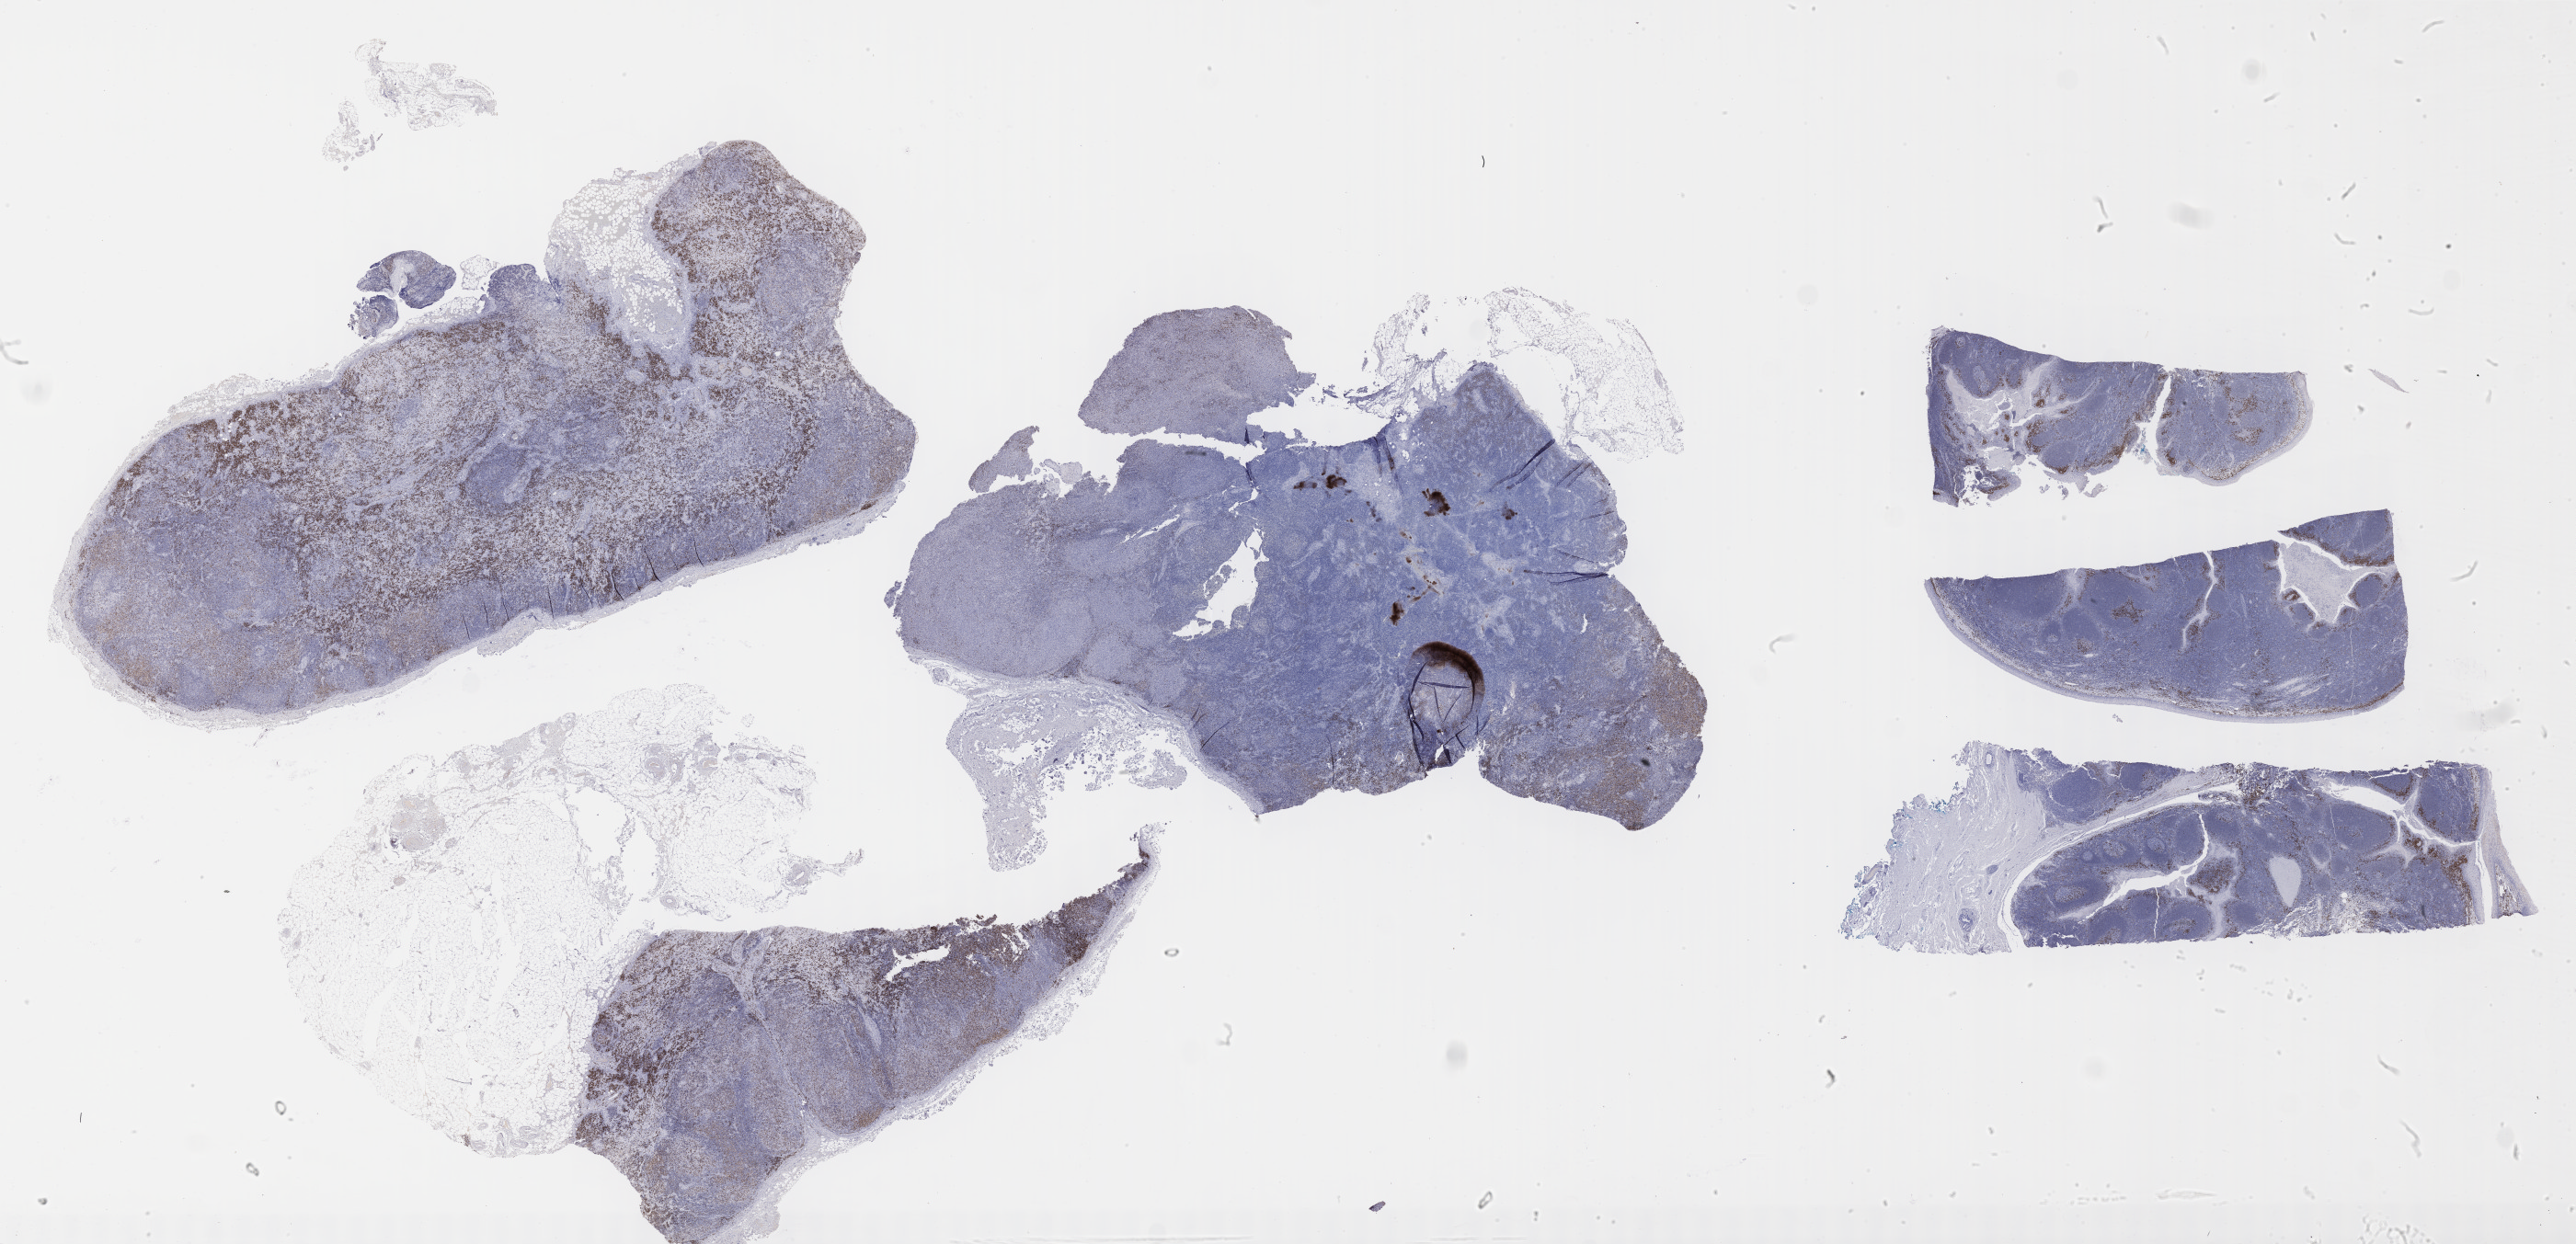
Whole-slide image, immunohistochemical stain for IRF4/MUM1 — whole scanned area (about 45.3 x 21.9 mm) shown as a low-resolution overview; specimen: tumor tissue; anatomic site: lymph node. Patient male; aged 56.
Histologic diagnosis: Diffuse large B-cell lymphoma, NOS.